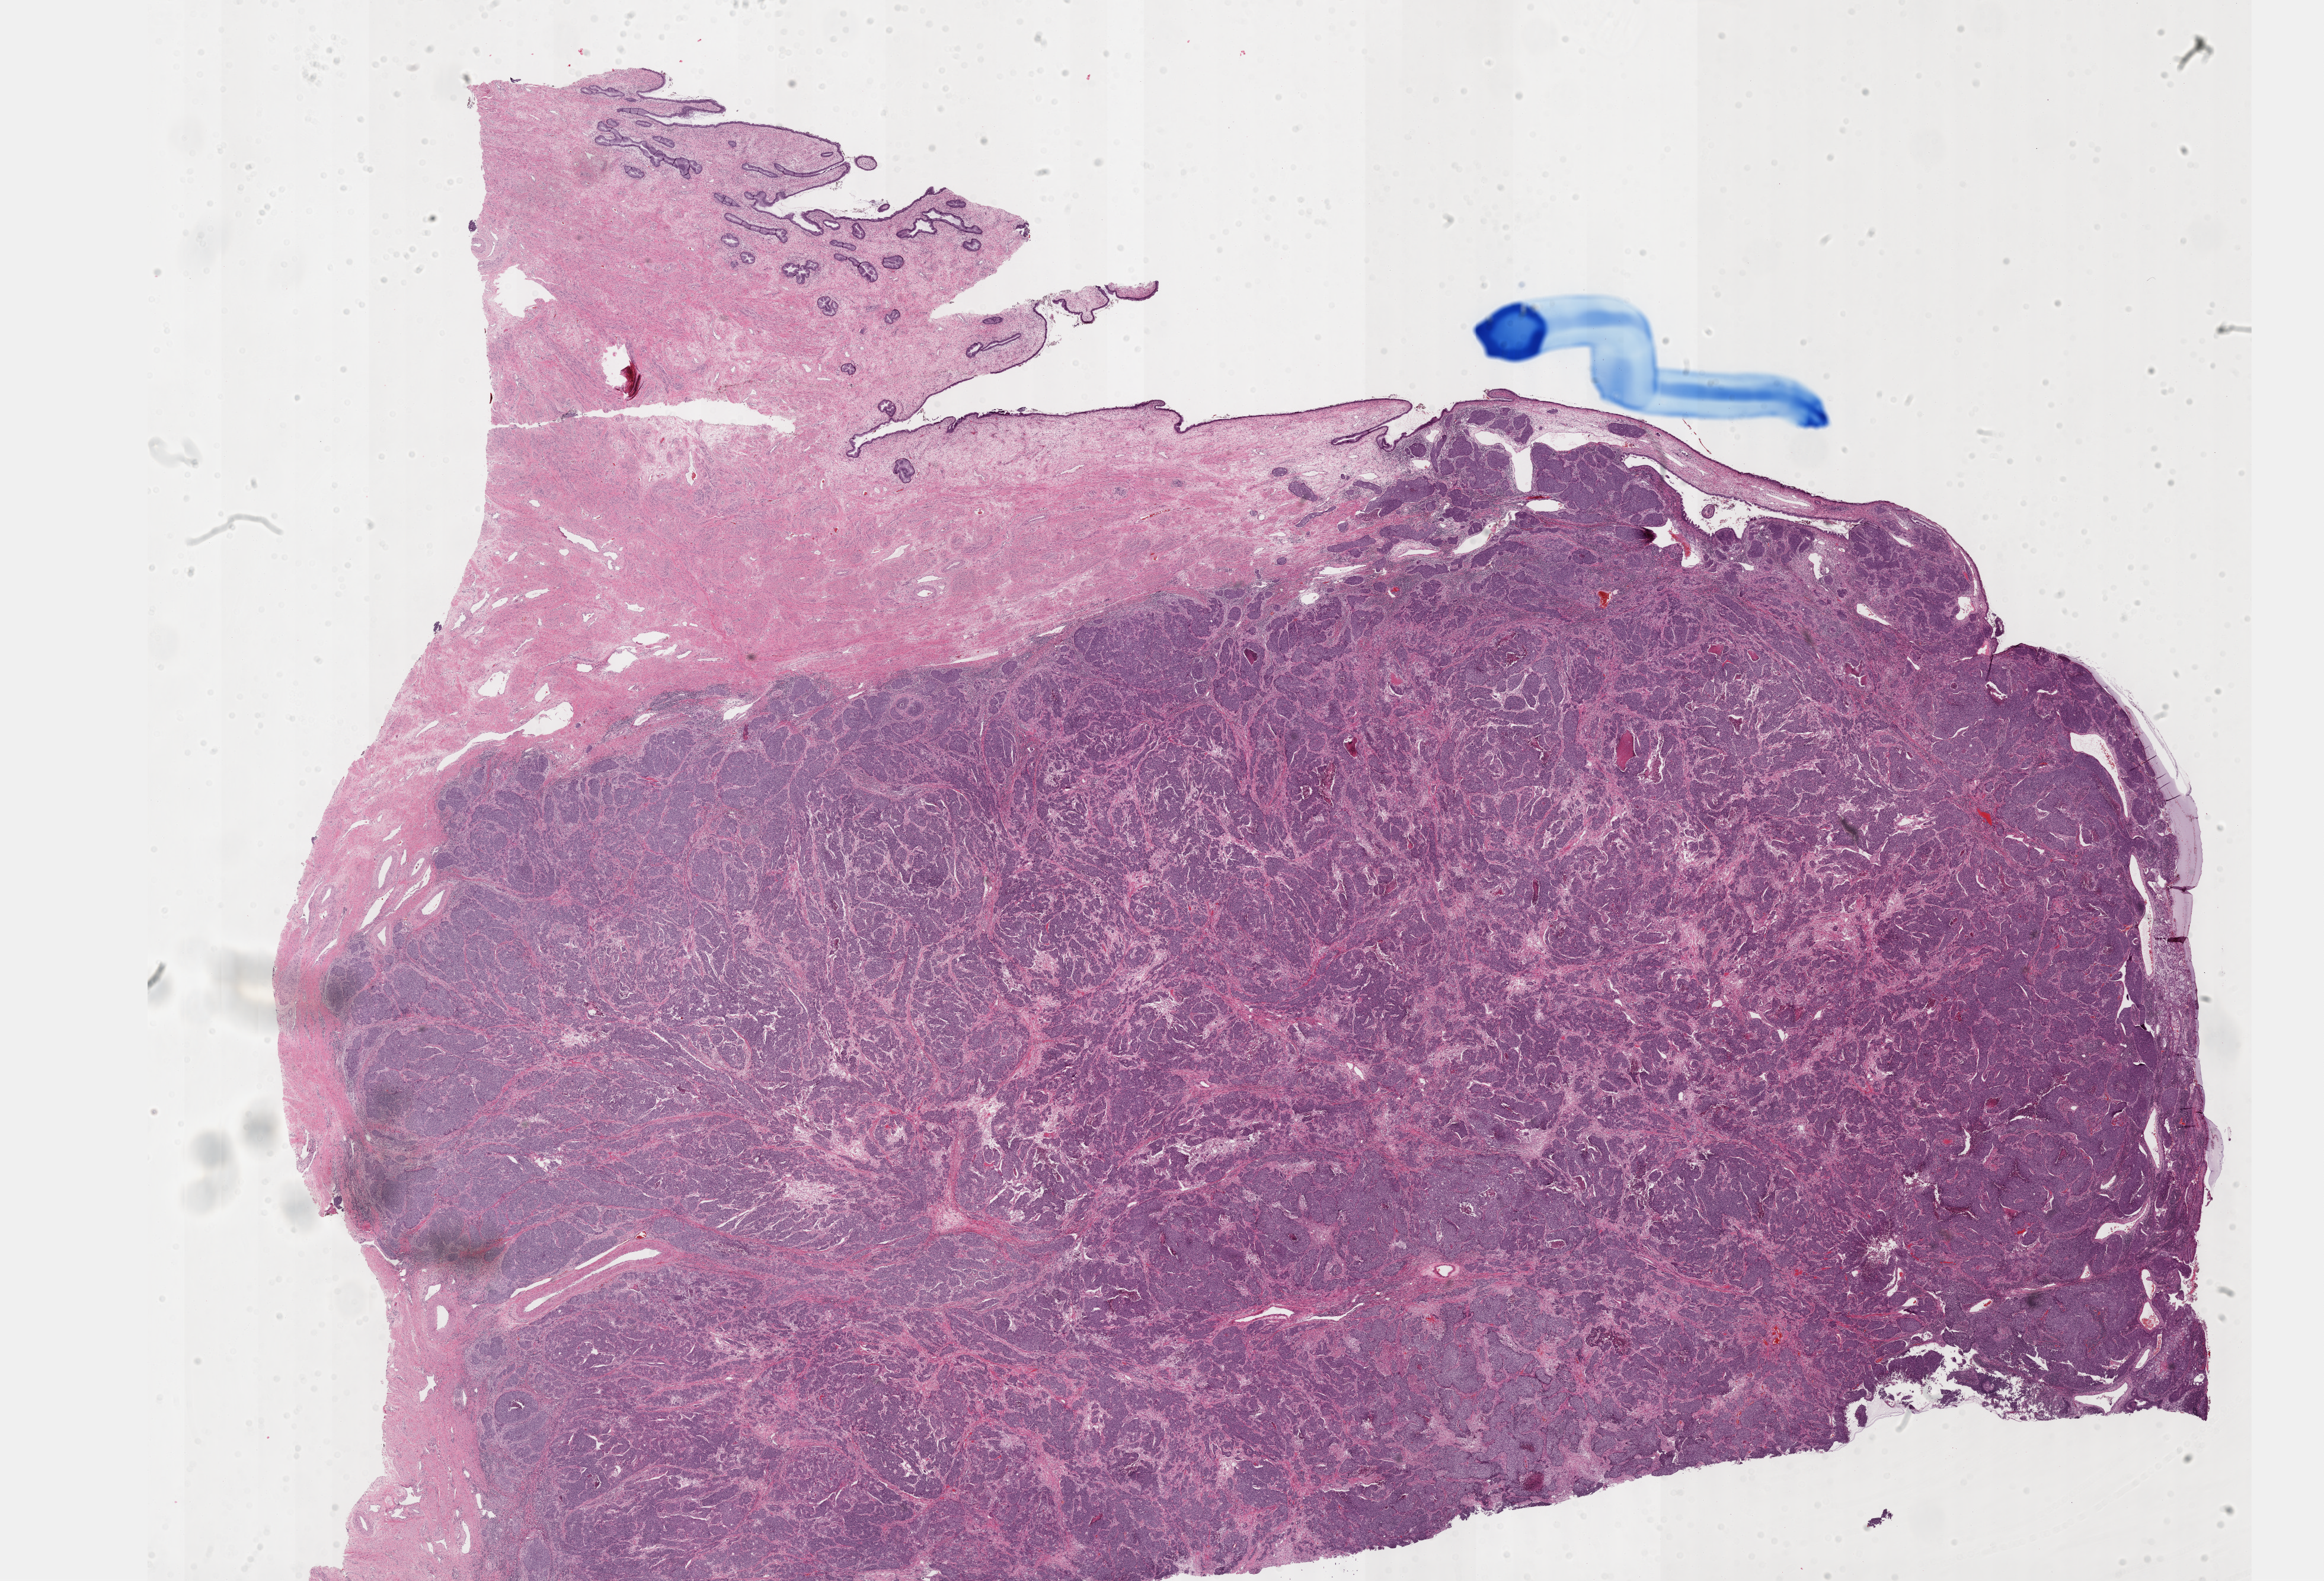
Hematoxylin and eosin (H&E) stained whole-slide image, low-resolution overview of the scanned area, about 31.7 x 21.6 mm; formalin-fixed paraffin-embedded (FFPE) diagnostic section; sample: primary tumour, cervix. Female patient; age at initial diagnosis 33 years. Histologic grade: G2 (moderately differentiated).
• FIGO stage: IB1
• pathologic diagnosis: Adenosquamous carcinoma (cervix uteri)